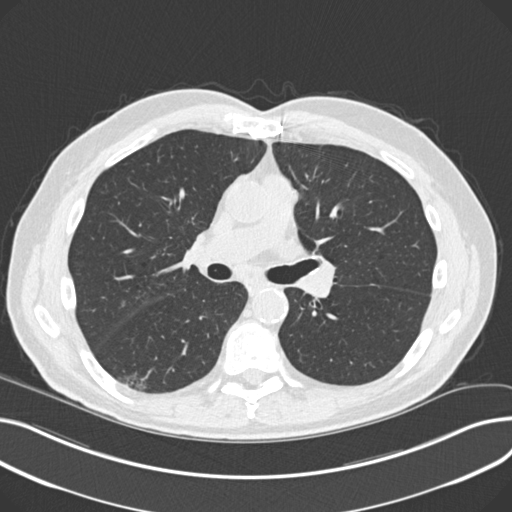
Low-dose screening chest CT, axial slice; third screening round (two years after baseline); lung window (W 1500 / L -600 HU). Male, age 68 years at enrolment. Current smoker at enrolment.
Lesion marked by an expert reader, bounding box [x1, y1, x2, y2] px = [122, 366, 163, 397]. The screening reader recorded 5 non-calcified nodules or masses ≥4 mm on this exam; which of them this box marks is not recorded. Official screen result: positive, other. Later outcome: lung cancer diagnosed 247 days after this screen — non-small cell carcinoma, right lower lobe, poorly differentiated (G3), stage IA (AJCC 6th edition), 23 mm at pathology.